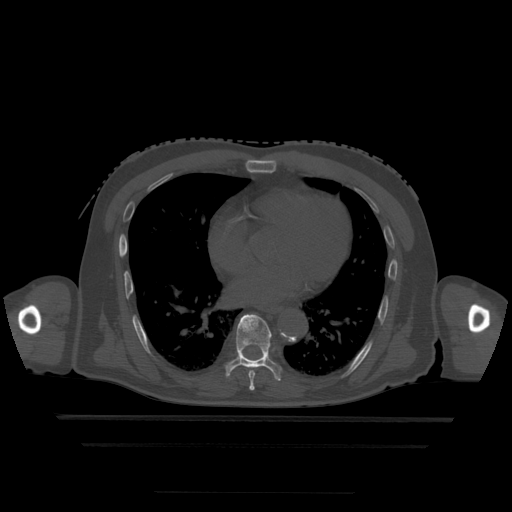
CT including the spine, one axial slice. Position 283 of 522 along the scan axis. Bone window (W 1800 / L 400 HU). 1.25 mm slice thickness. 512 × 512 image matrix, field of view 436 × 436 mm. Patient age 68 years. From the clinical record (not read from this slice): primary cancer: urothelial.
Annotated regions visible in this slice (semi-automatically segmented with operator editing):
- T7 vertebra: box from (x=249, y=371) to (x=255, y=391) px
- T8 vertebra: (x=225, y=314)–(x=282, y=381)